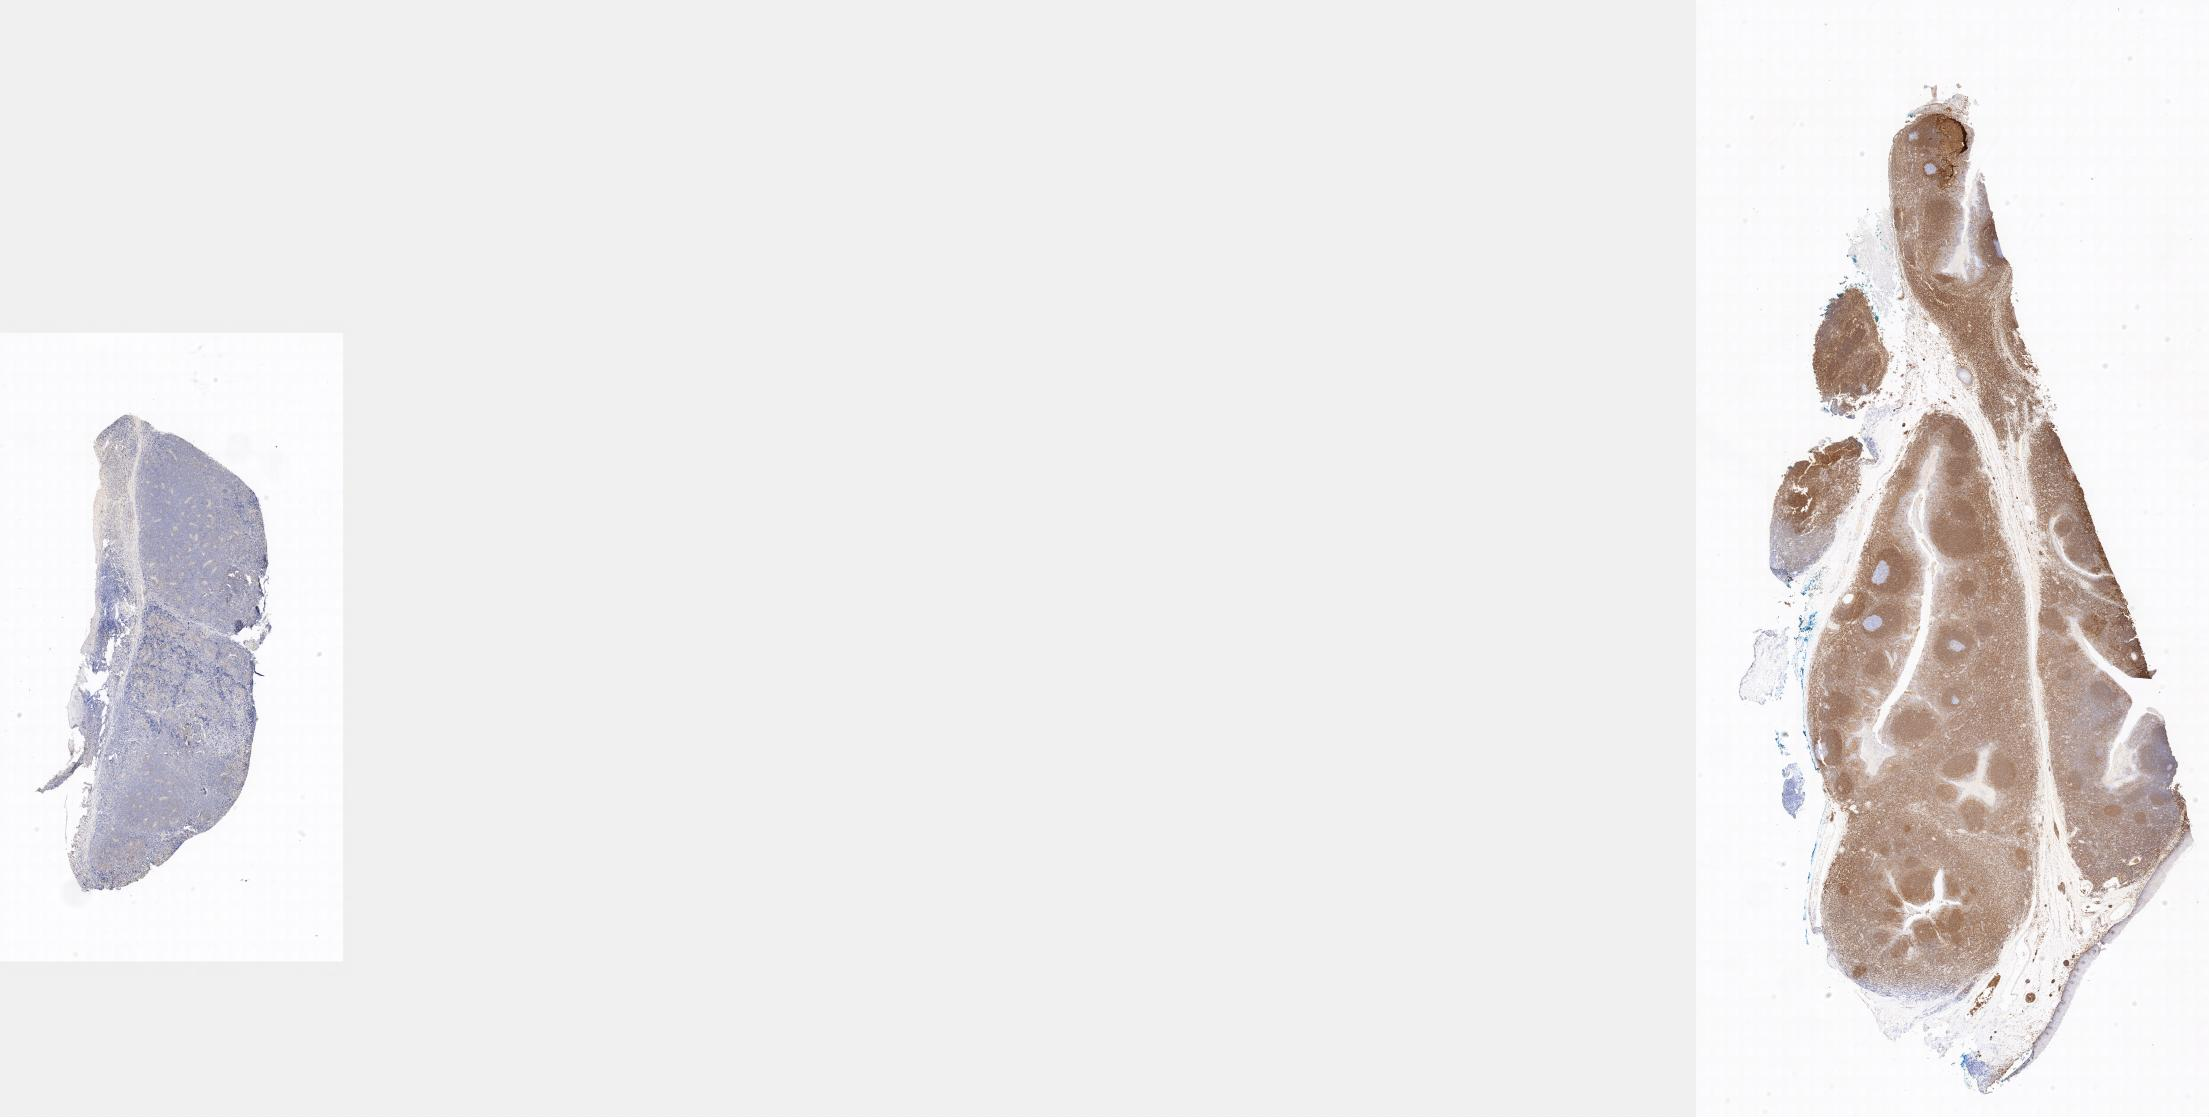
Whole-slide image, immunohistochemical stain for BCL2, a low-resolution overview of the entire scanned area. Tumor tissue. Anatomic site: testis. Patient: male, age at initial diagnosis 8 years.
Diagnosis: Burkitt lymphoma, NOS.